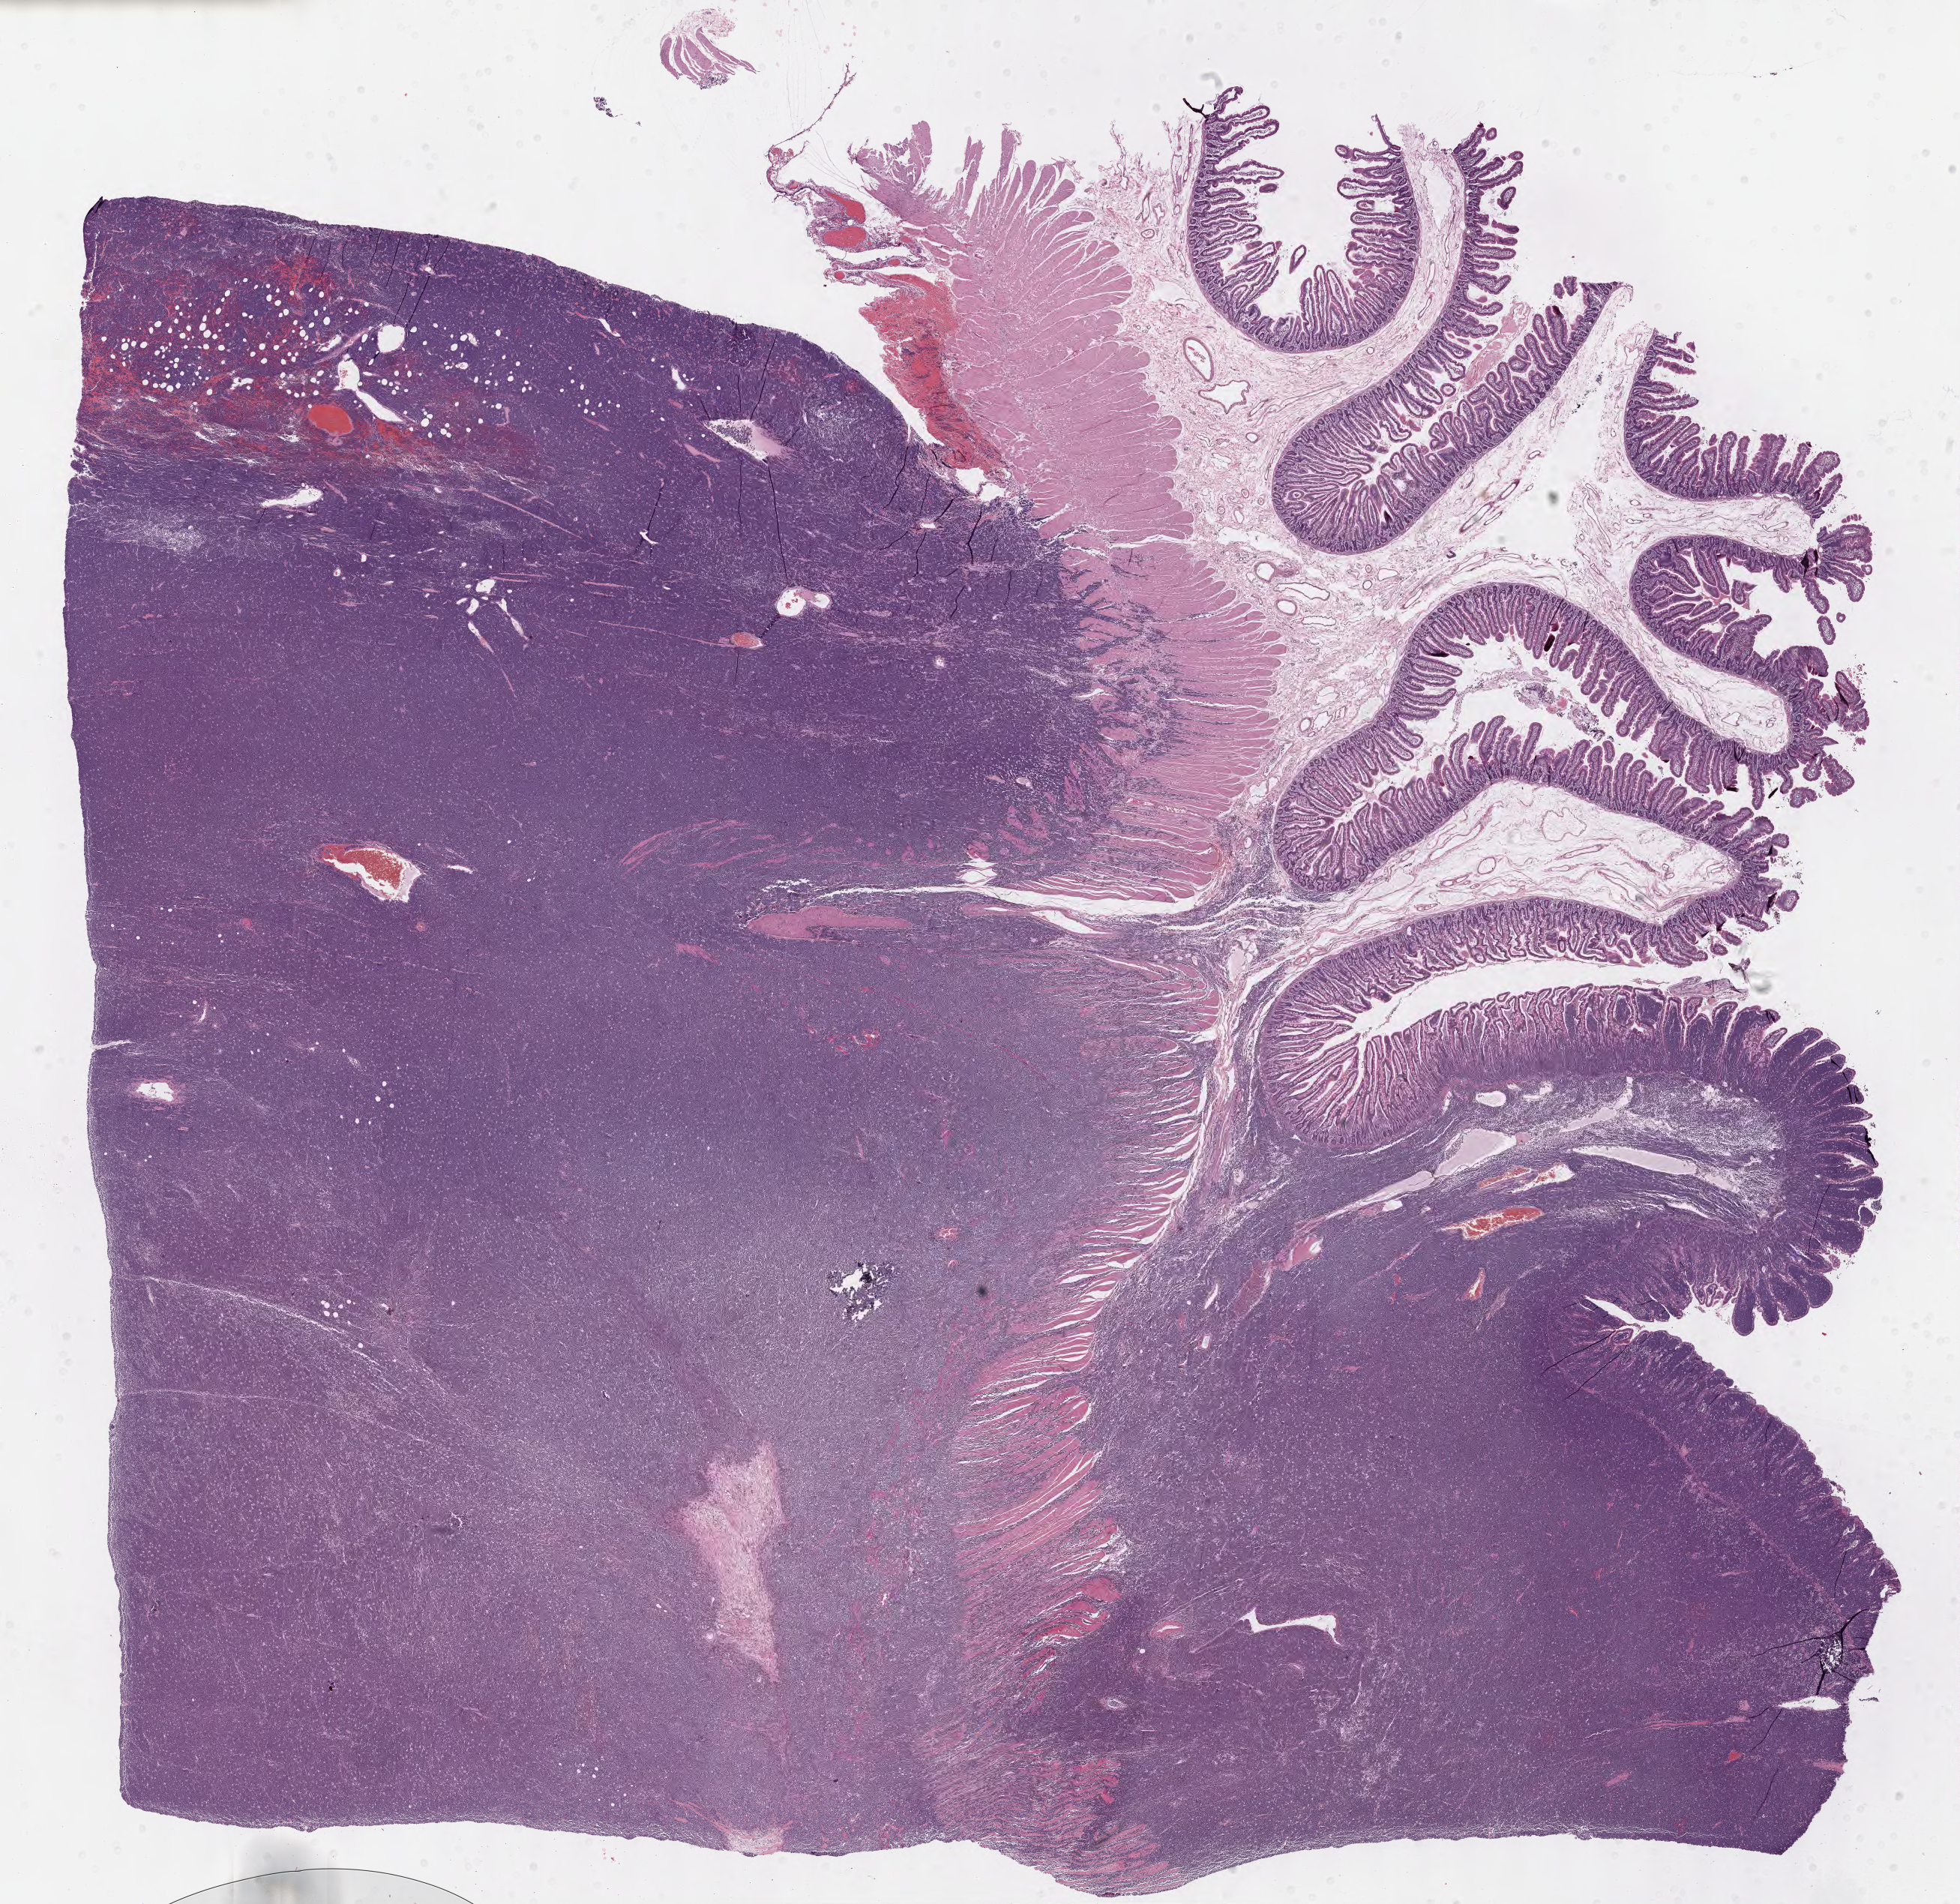
Digitized H&E-stained section — whole scanned area (about 21.1 x 20.5 mm) shown as a low-resolution overview. Tumor tissue. Patient male; 36 years old.
Histologic diagnosis: Burkitt lymphoma, NOS.